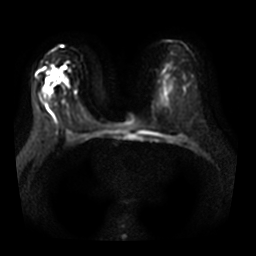
Breast MRI, one axial slice. Slice 20 of 32 in the series (ordered by position). Diffusion-weighted series; image 2 of 4 stored at this slice position (different b-values; order by instance number). 3 T. 5 mm slice thickness. 256 × 256 image matrix, field of view 350 × 350 mm. Female patient.
Structures marked on this image (manually delineated by an expert):
- tumour on diffusion-weighted imaging: bounding box [x1, y1, x2, y2] px = [48, 69, 60, 80]